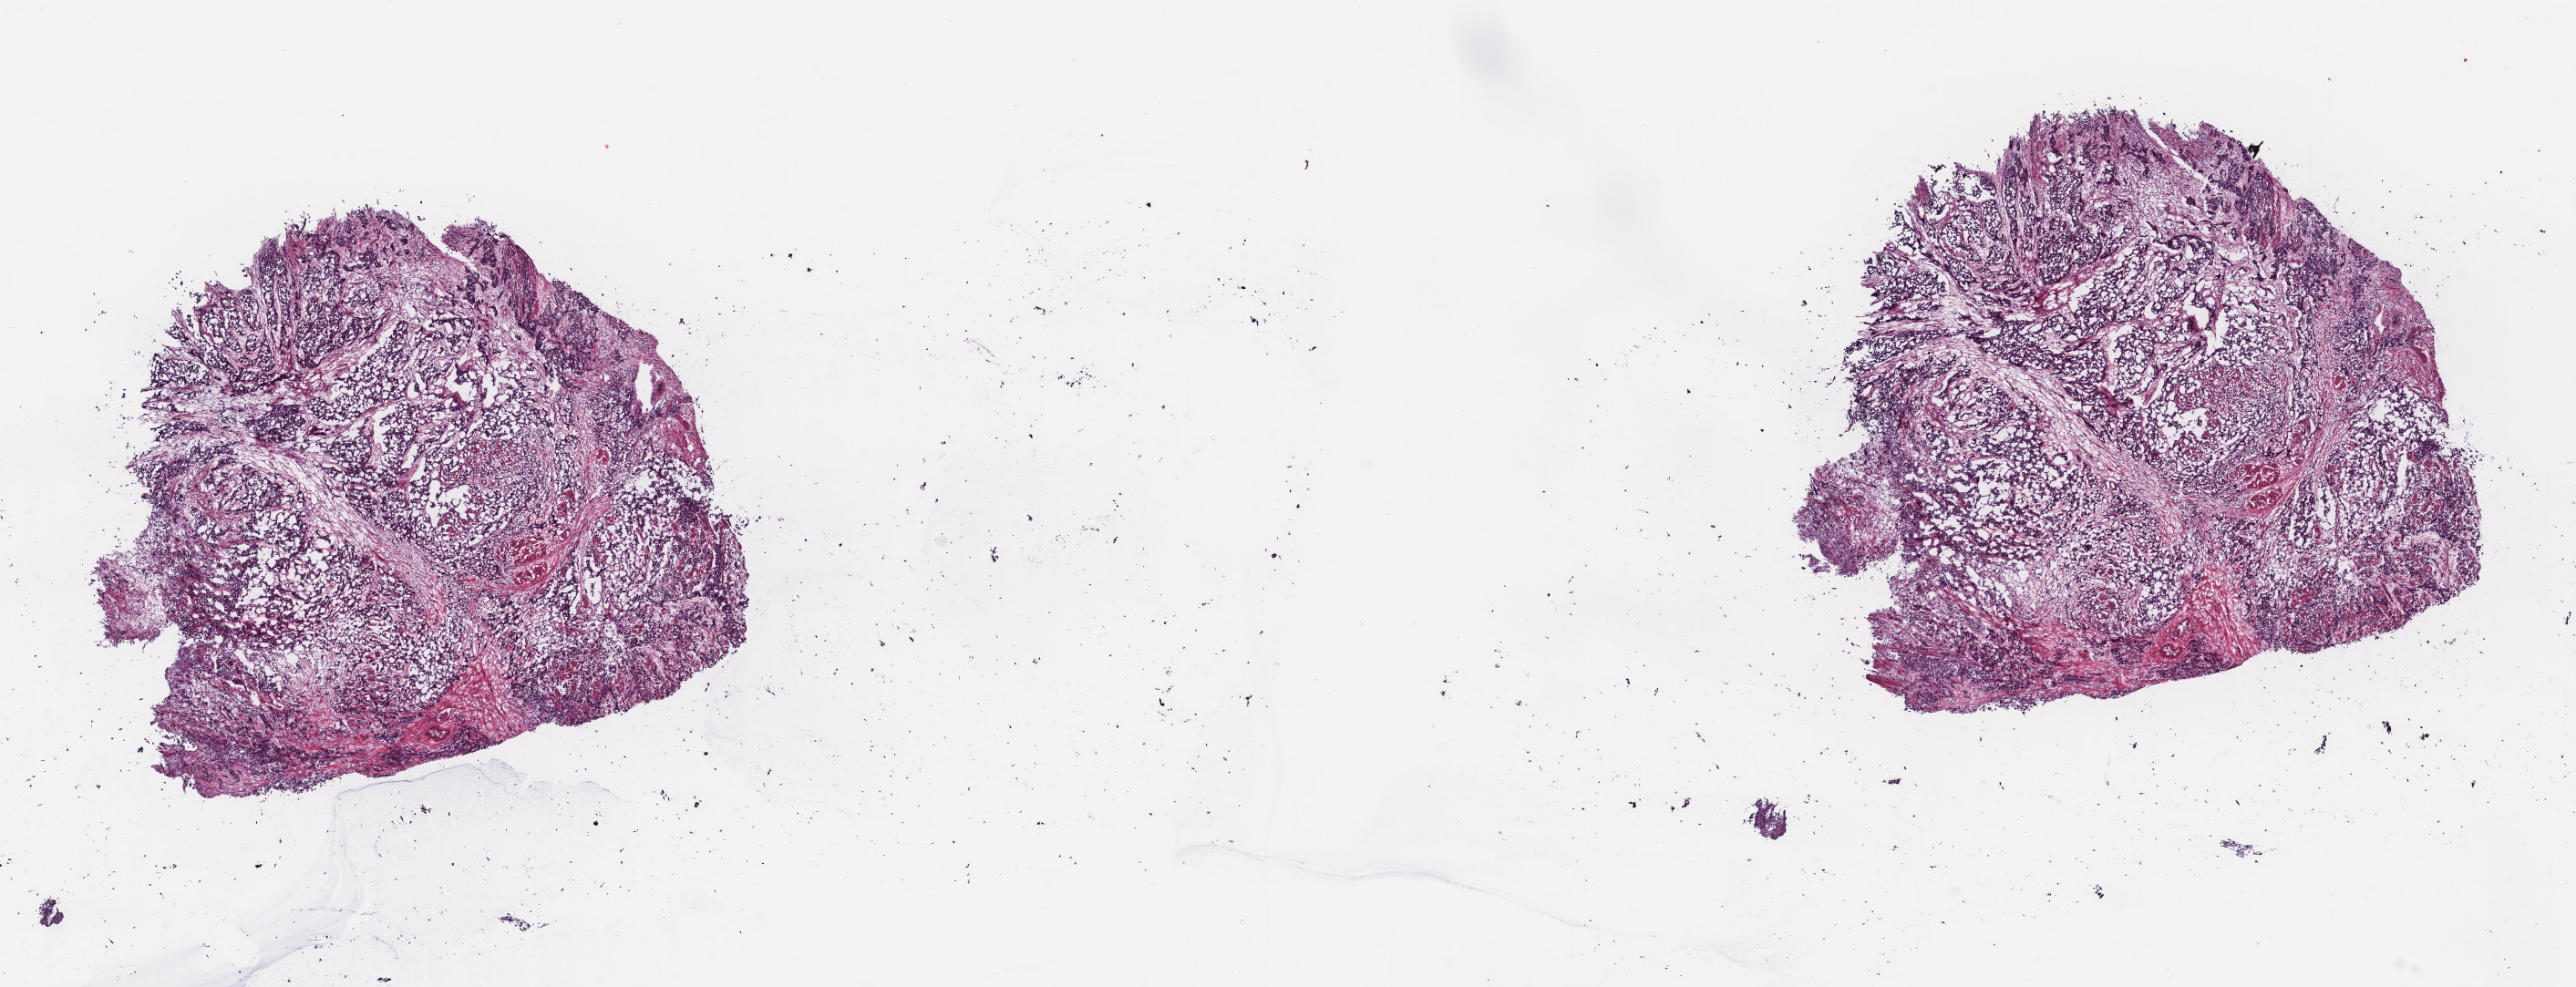
Whole-slide histology image, Hematoxylin and eosin (H&E) stained, low-resolution overview of the scanned area, about 22.3 x 8.5 mm (from a 40x scan); frozen section from the top of the tissue portion; bladder, primary tumour sample. Male patient; age at initial diagnosis 63 years. Histologic grade: high grade. Slide review estimates, as recorded: tumour cells 75%, tumour nuclei 75%, normal cells 0%, stromal cells 25%, necrosis 0%. Inflammatory infiltration, as recorded: lymphocyte infiltration 3%, monocyte infiltration 0%, neutrophil infiltration 0%.
AJCC pathologic stage: IV (6th edition). Pathologic diagnosis: Transitional cell carcinoma (anterior wall of bladder). Lymph nodes positive (case pathology): 1 of 6 examined.